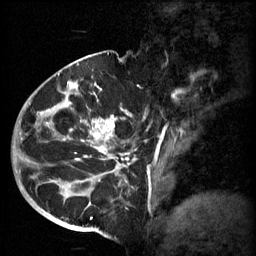
Breast MRI (dynamic contrast-enhanced), one sagittal slice. Position 36 of 60 along the scan axis. 3 images stored at this slice position (order not interpretable as contrast timing). 1.5 T. TE 4.2 ms, TR 11 ms. 2 mm slice thickness. 256 × 256 image matrix, field of view 200 × 200 mm. Patient: female, 51 years.
Annotated regions visible in this slice (semi-automatically segmented with operator editing):
- analysis volume of interest (the breast-tissue region the enhancement analysis was run in; not a lesion): bounding box <48,82,161,197> (left, top, right, bottom; pixels)
- tumour enhancement mask (voxels above the 70 % enhancement threshold inside the analysis volume of interest): <48,82,131,195>